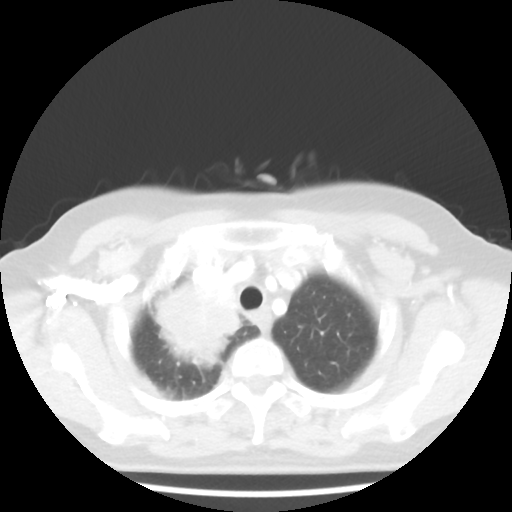
Chest CT, one axial slice. Reconstruction kernel STANDARD. Lung window (W 1500 / L -600 HU). 5 mm slice thickness. 512 × 512 image matrix. Female patient, age 62 years. From the clinical record (not read from this slice): clinical TNM (as recorded): T3 N0 M0; histopathological grade: G3.
Annotated regions visible in this slice (bounding box drawn by a radiologist):
- lung tumour (recorded histology: small cell carcinoma): bounding box [x1, y1, x2, y2] px = [139, 262, 248, 372]